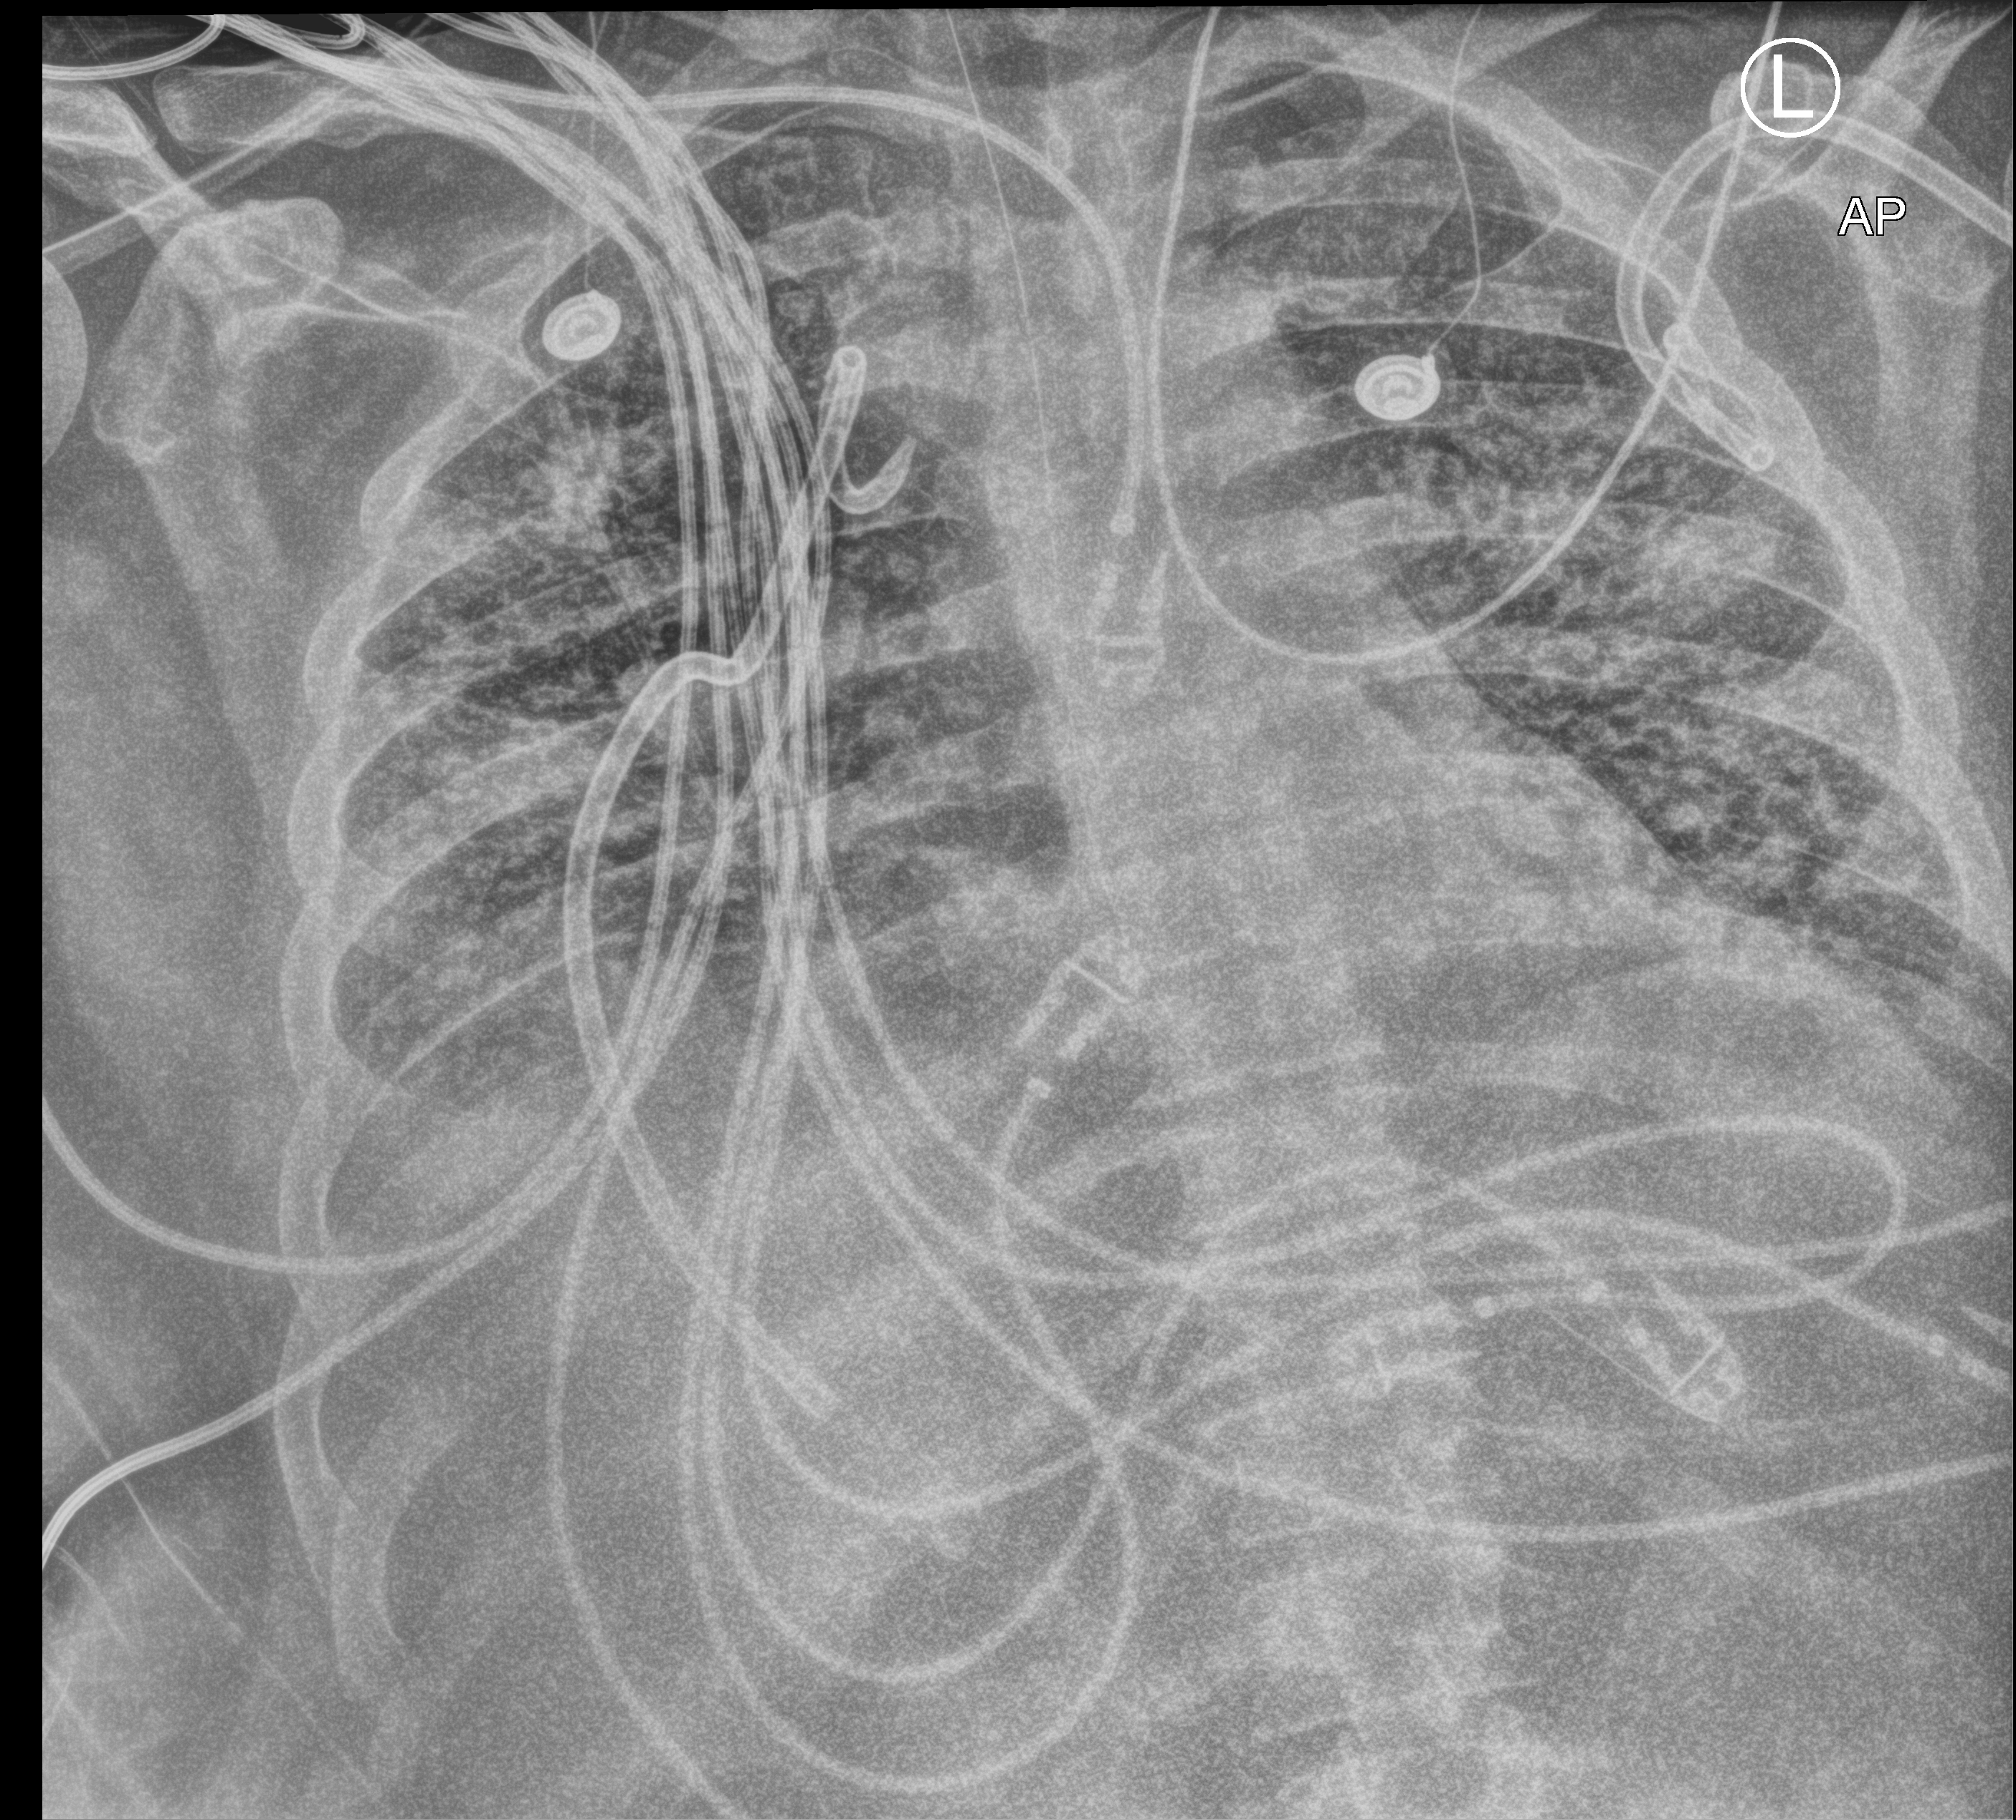
Portable chest radiograph; anteroposterior (AP) projection. Patient hospitalised with COVID-19, aged 18–59 years.
Admission-level facts for this patient (not findings on this image; timing relative to this image not recorded):
- mechanically ventilated during this hospital stay: yes
- admitted to intensive care during this hospital stay: yes
- length of hospital stay: 31 days